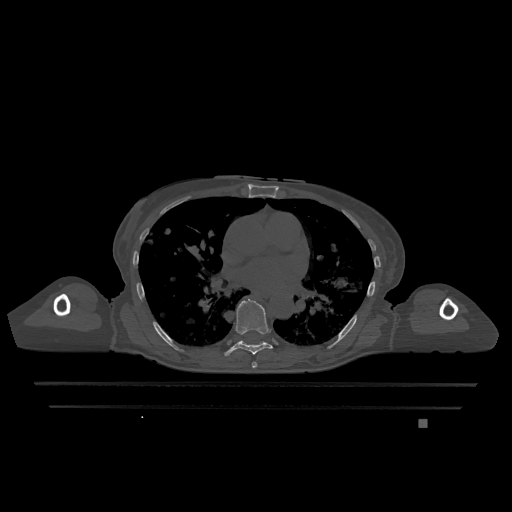
CT including the spine, one axial slice; position 736 of 1317 along the scan axis; bone window (W 1800 / L 400 HU); 512 × 512 image matrix, field of view 500 × 500 mm. Female patient, age 74 years. Case-level facts recorded for this patient, not image findings: primary cancer: lung; vertebrae with lytic lesions (as recorded): T1, T4, T5, T6, L4, L5.
Annotated regions visible in this slice (semi-automatic segmentation, software-assisted and operator-edited):
- T6 vertebra: box from (x=252, y=361) to (x=258, y=368) px
- T7 vertebra: (x=224, y=299)–(x=273, y=356)